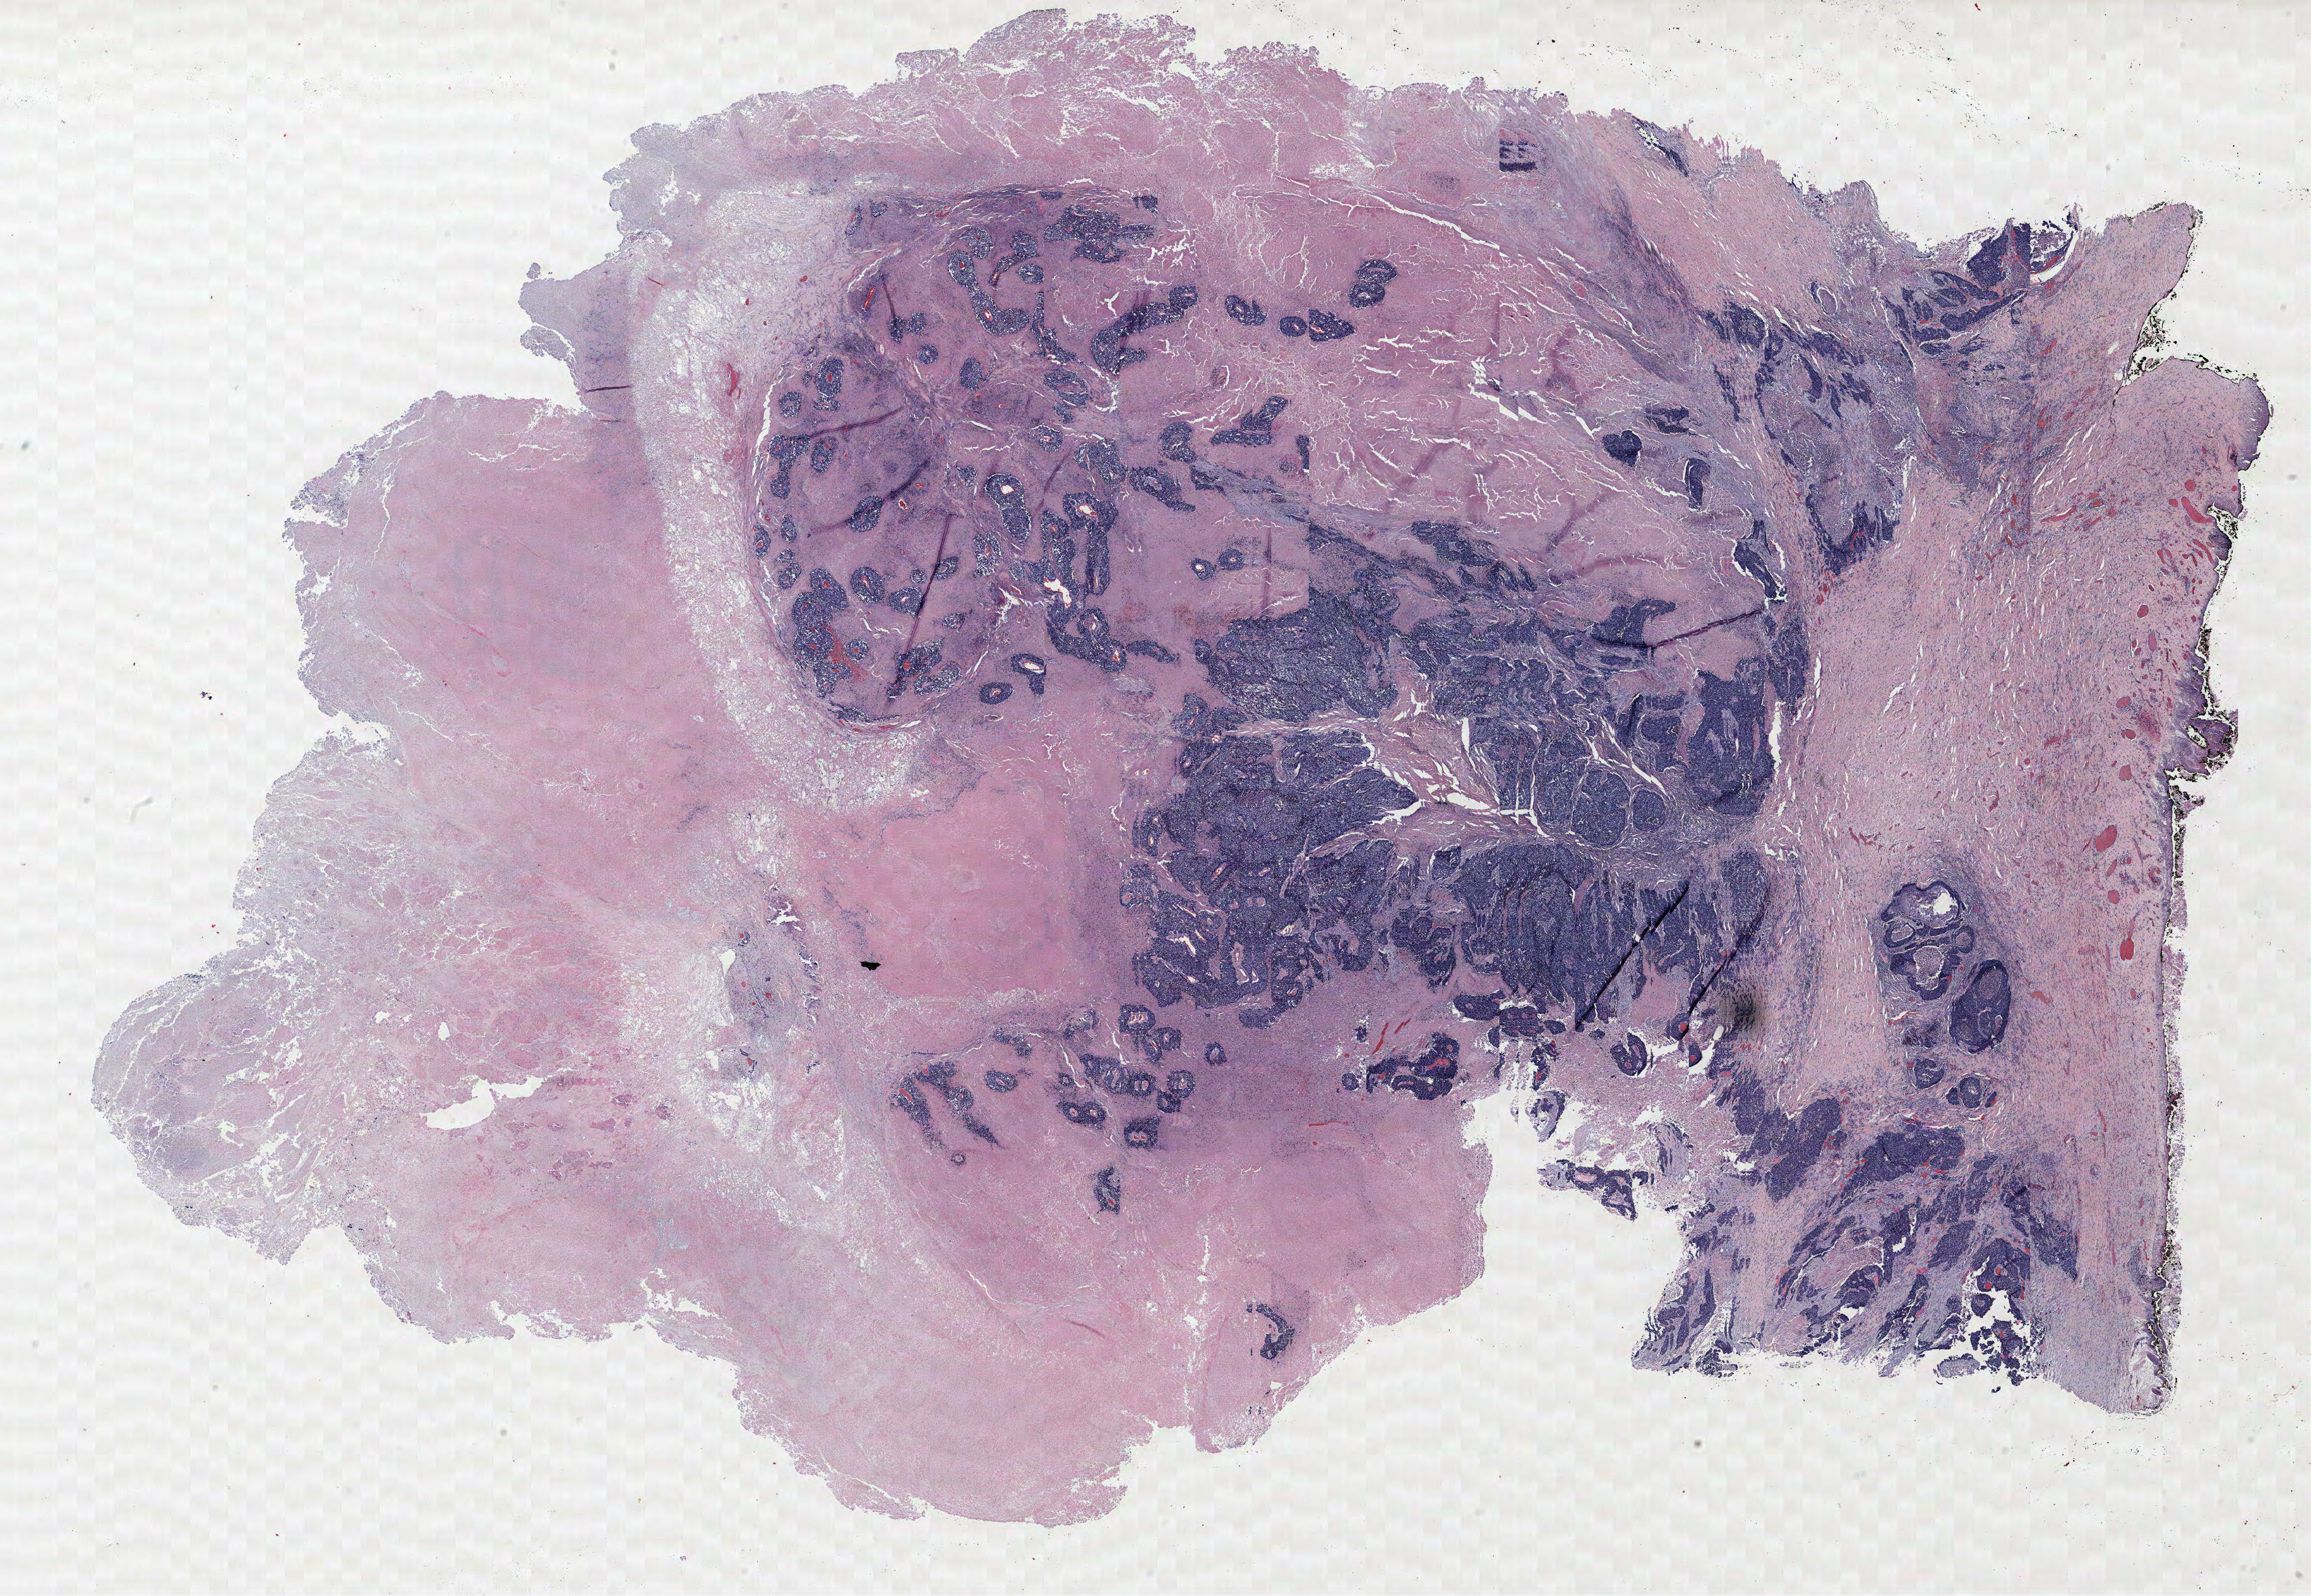
Hematoxylin and eosin (H&E) stained whole-slide image — low-resolution overview of the scanned area, about 29.3 x 20.2 mm (acquisition: 40x scan). FFPE section. Lung tissue. Male, age 65 at enrolment. Current smoker at enrolment. Grade: poorly differentiated (G3).
Participant's lung-cancer diagnosis: Adenocarcinoma, NOS (ICD-O-3 8140/3). Primary tumour location (clinical record): right upper lobe. Tumour size (pathology): 13 mm. Stage (AJCC 6th edition): IB. Note: participant had 2 primary lung cancers recorded; fields above describe the first.